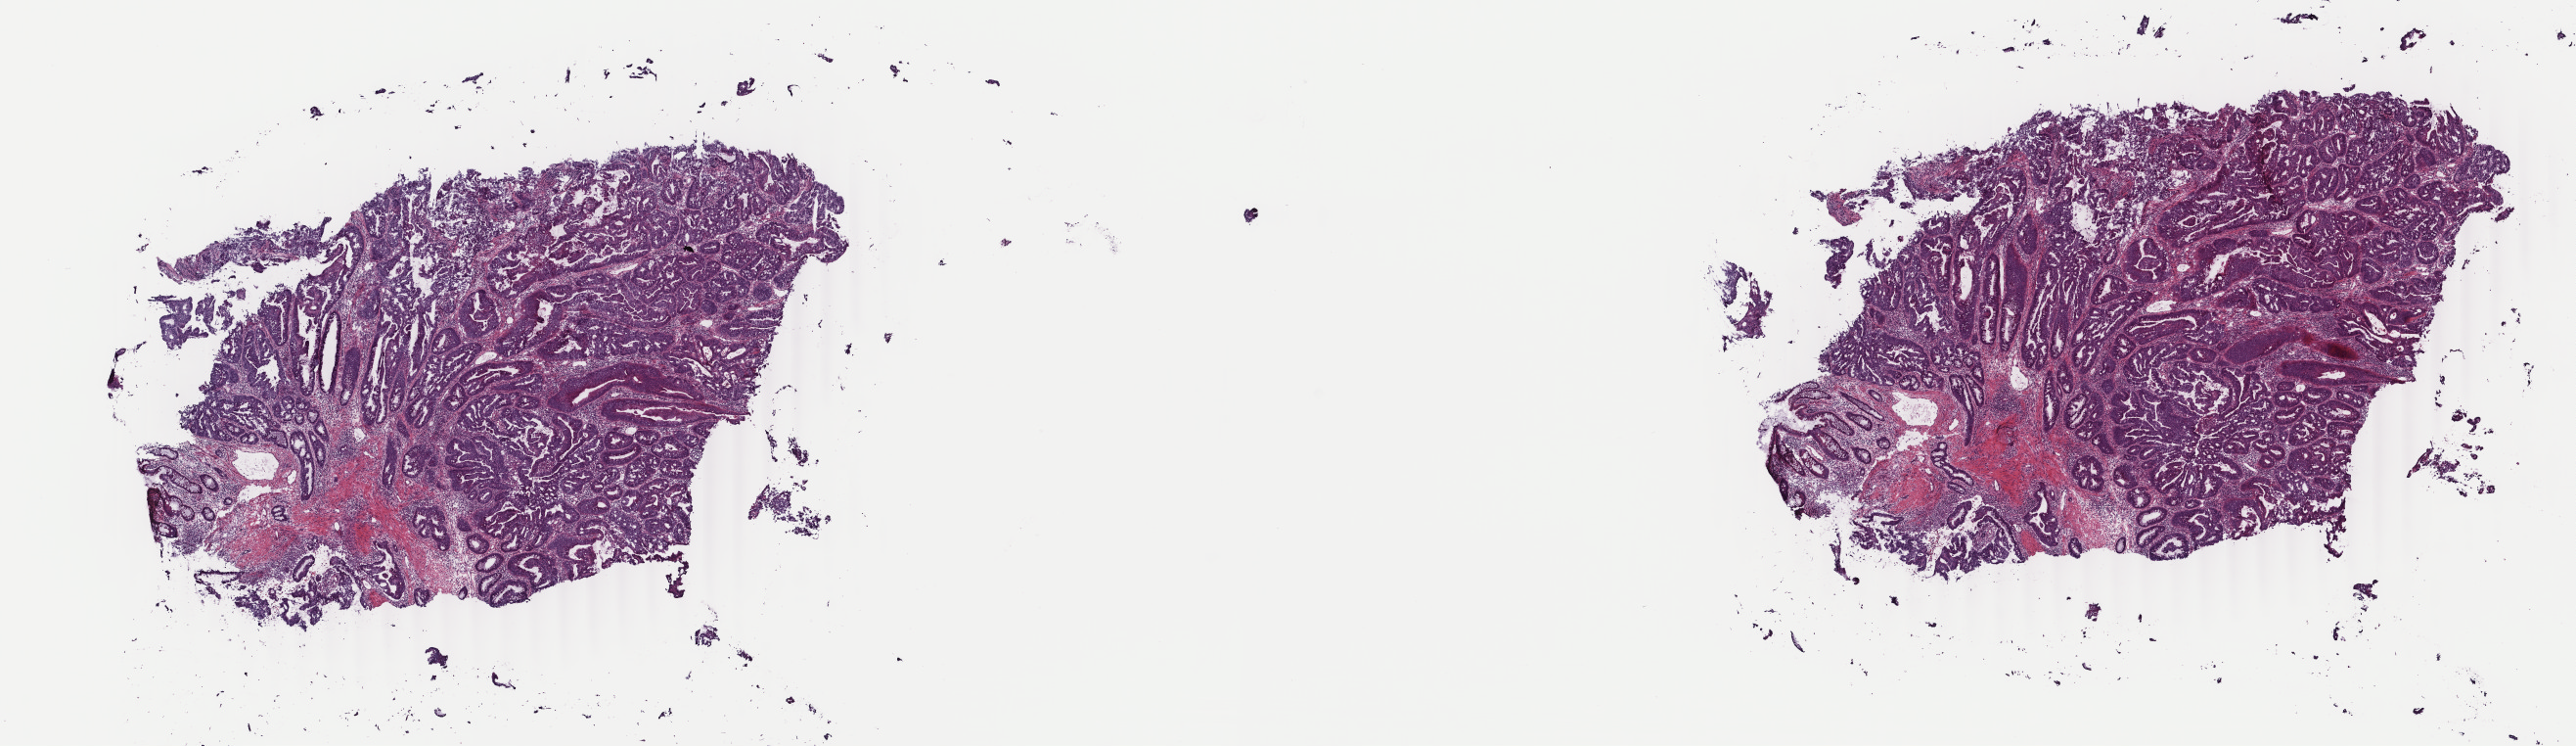
Hematoxylin and eosin (H&E) stained whole-slide image, low-resolution overview of the scanned area, about 20.9 x 6.1 mm. Frozen section from the top of the tissue portion. Sample: primary tumour, colon. Female, age 61 years at initial diagnosis.
Pathologic diagnosis: Adenocarcinoma, NOS (sigmoid colon).